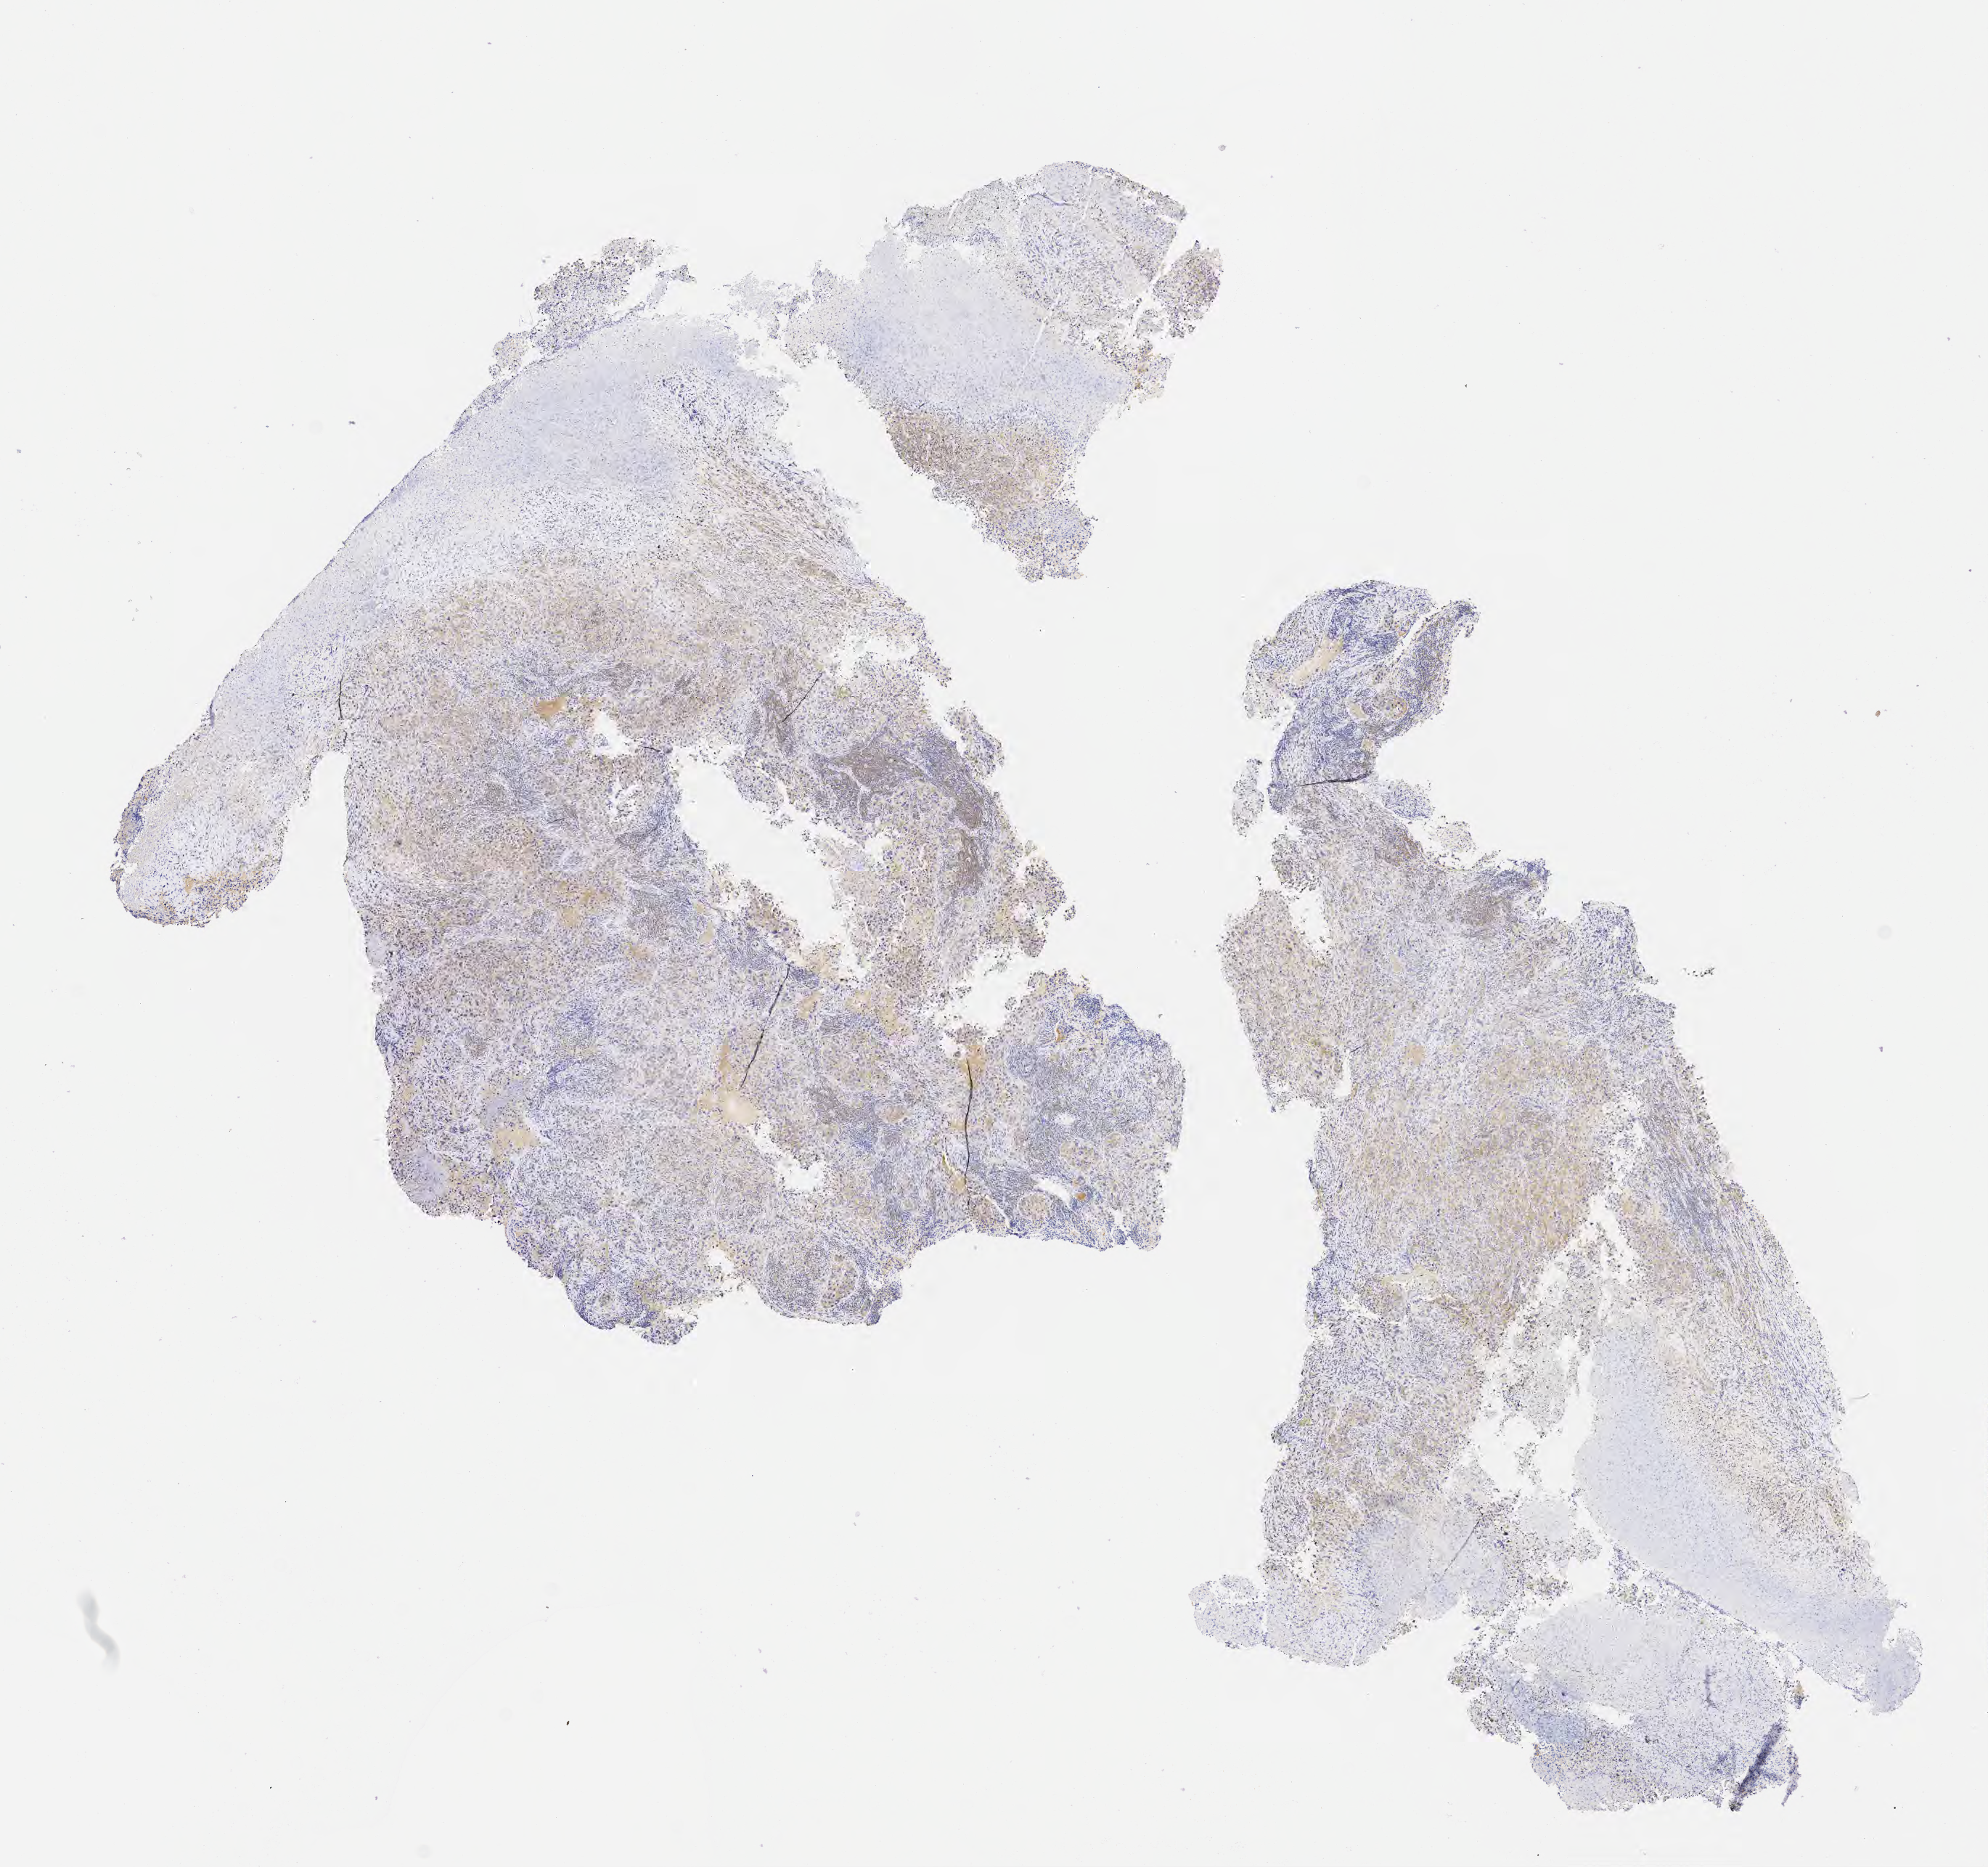
Whole-slide image, immunohistochemical stain for p63, a low-resolution overview of the entire scanned area, about 11.1 x 10.4 mm. Specimen: tumor tissue. Anatomic site: cervix. Patient: female, 38 years old.
* diagnosis: Squamous cell carcinoma, large cell, nonkeratinizing, NOS